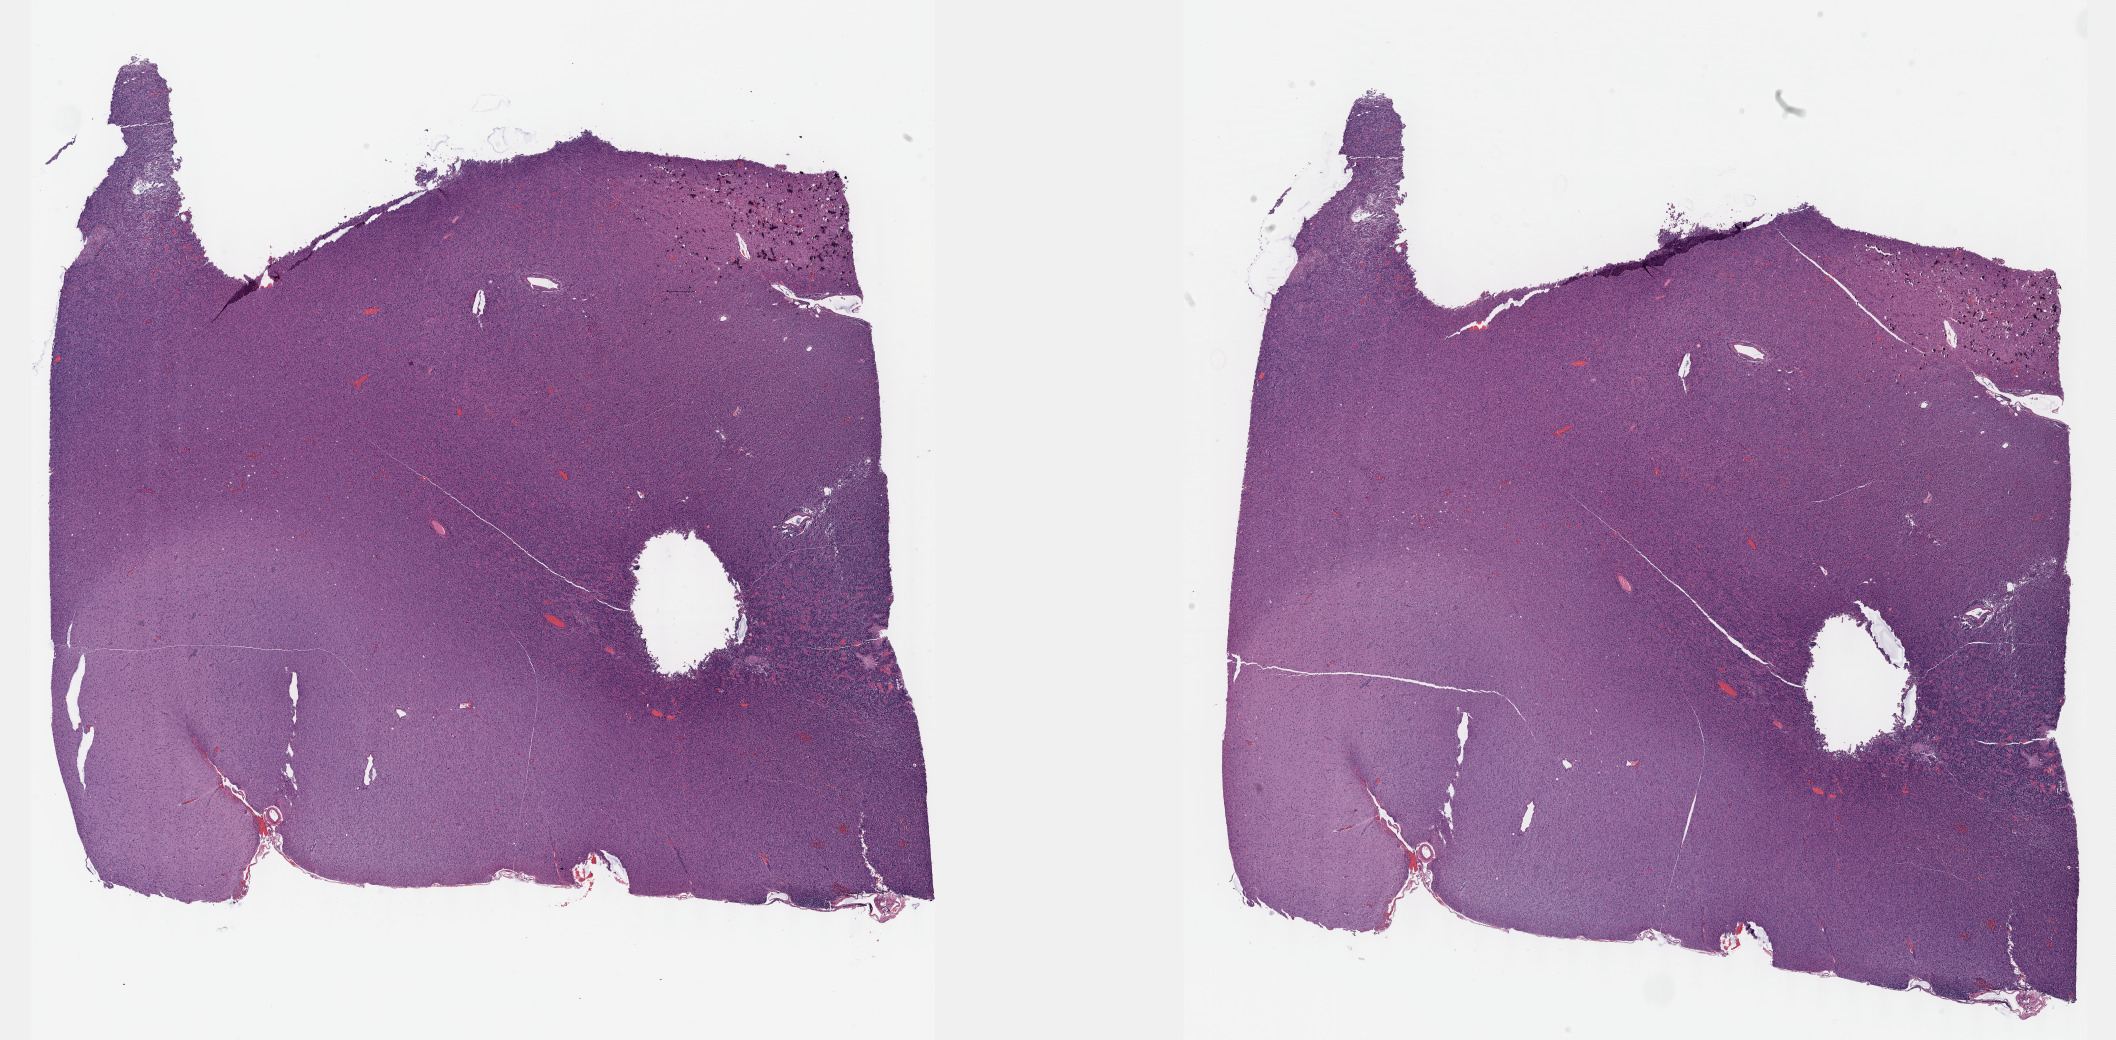
Digitized Hematoxylin and eosin (H&E) stained tissue section (whole slide) — low-resolution overview of the scanned area, about 34.2 x 16.8 mm (from a 40x scan), formalin-fixed paraffin-embedded (FFPE) diagnostic section, primary tumour sample from the brain. Male, age 40 years at initial diagnosis.
Pathologic diagnosis: Glioblastoma.